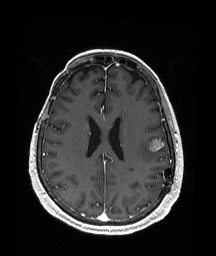
Brain MRI from a brain-tumour surgery series, one axial slice. Slice 74 of 176 in the series (ordered by position). T1-weighted post-contrast. 1 mm slice thickness. 216 × 256 image matrix, field of view 211 × 250 mm. Case-level facts recorded for this patient, not image findings: histopathology: Metastatic Malignant Melanoma.
Structures marked on this image (expert manual segmentation):
- tumour: box from (x=148, y=138) to (x=164, y=152) px